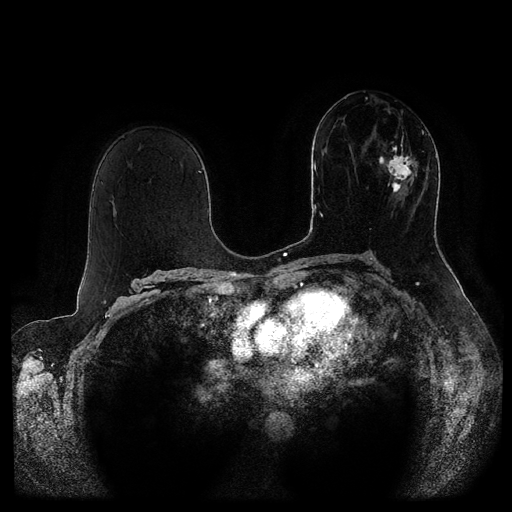
Breast MRI (dynamic contrast-enhanced, multi-phase), one axial slice; position 55 of 116 along the scan axis; dynamic contrast-enhanced series, time point 2 of 5 at this slice position (early post-contrast); 1.5 T; TE 2.6 ms, TR 5.3 ms; 2 mm slice thickness; 512 × 512 image matrix, field of view 370 × 370 mm. Female patient, age 51 years.
Annotated regions visible in this slice (semi-automatic segmentation, software-assisted and operator-edited):
- breast lesion (labelled 'tumour' in the annotation; benign lesions carry a separate 'benign' label): bounding box [x1, y1, x2, y2] px = [379, 119, 427, 193]